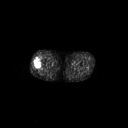
FDG PET of an extremity soft-tissue mass (from a PET/CT study), one axial slice. Position 234 of 267 along the scan axis. 3.27 mm slice thickness. 128 × 128 image matrix, field of view 700 × 700 mm. Patient: male, 43 years. From the clinical record (not read from this slice): histological type: poorly differentiated synovial sarcoma; grade: high; site of the primary tumour: right buttock.
Outlined on this slice (expert contour drawn on MRI and transferred to this co-registered scan by the dataset authors):
- gross tumour volume including surrounding oedema: bounding box [x1, y1, x2, y2] px = [33, 57, 42, 70]
- gross tumour volume (mass): [34, 59, 42, 70]